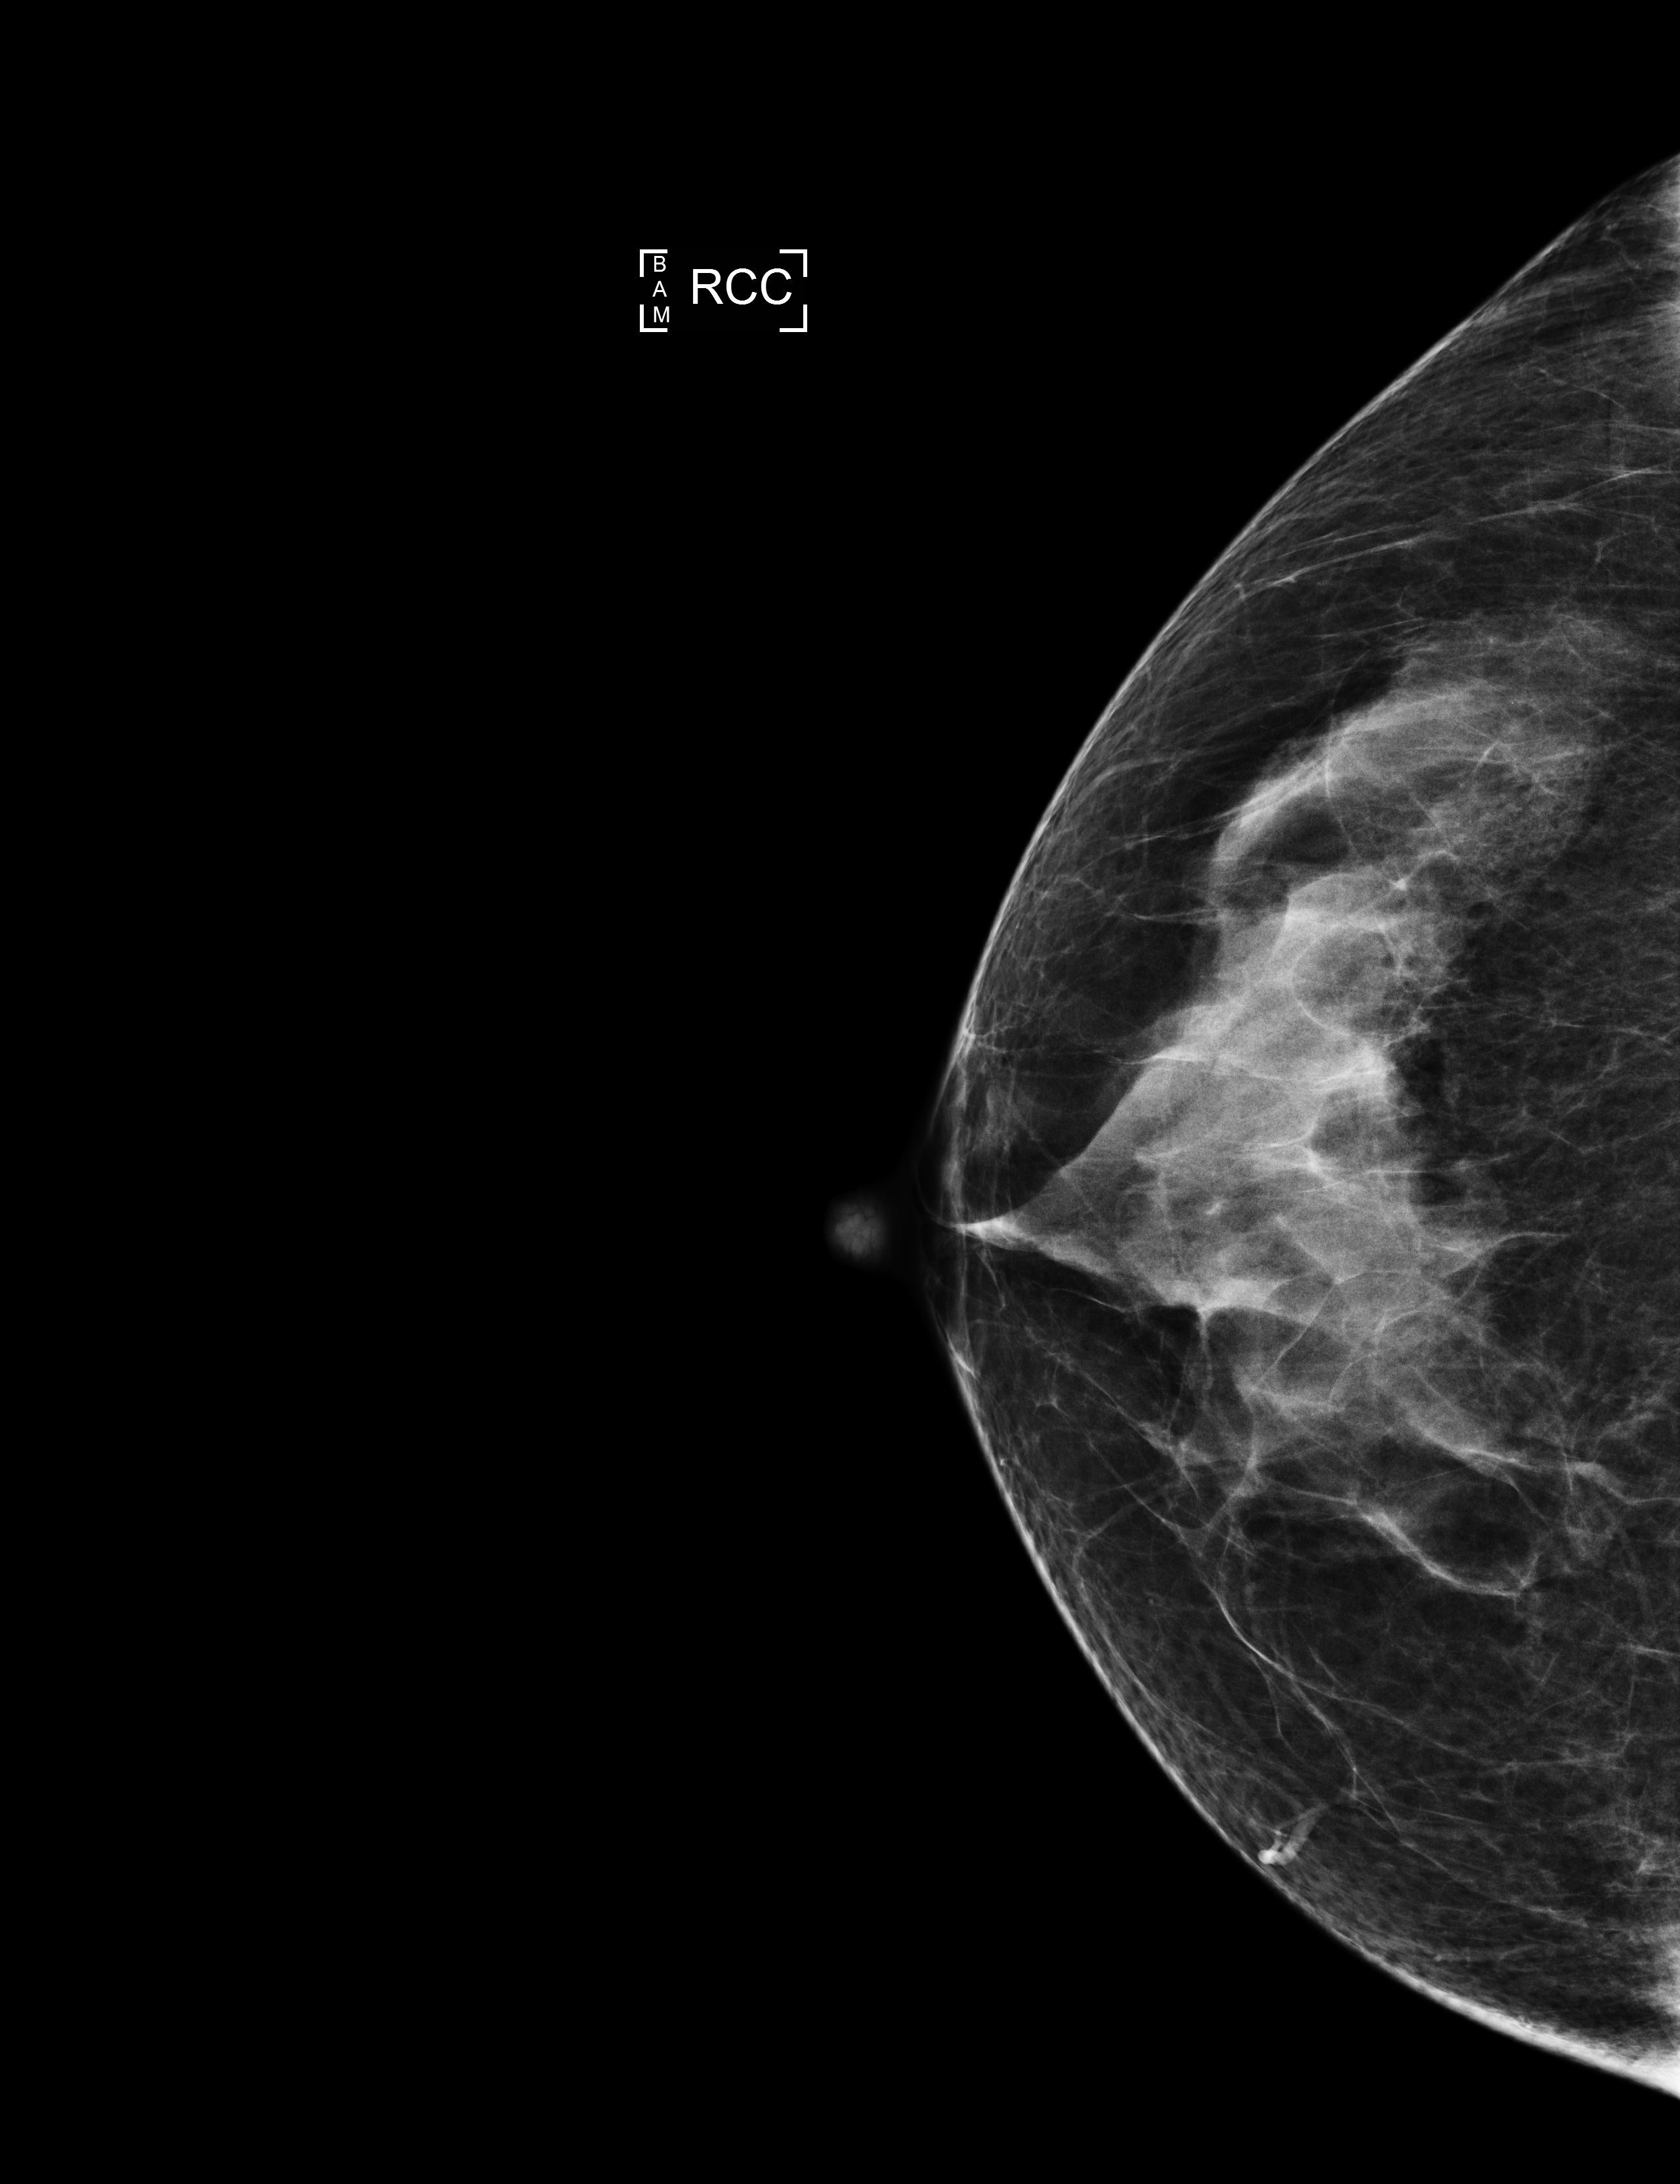
Digital mammogram (FFDM); right breast; craniocaudal (CC) view; annual screening mammography examination; compressed breast thickness 64 mm. Female patient, age 59 years.
Final BI-RADS category for the screening round (tomosynthesis exam, both breasts): category 1.